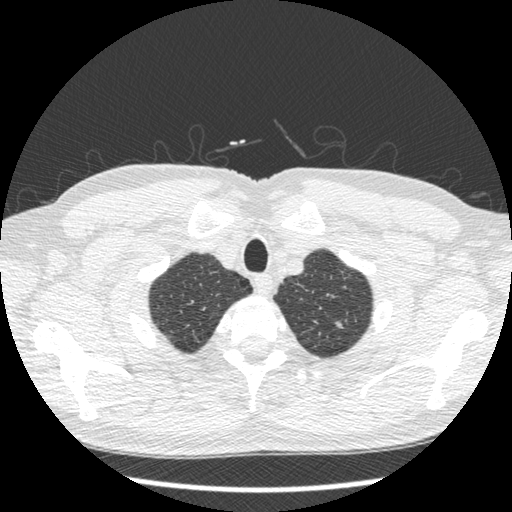
Low-dose screening chest CT, one axial slice. Position 405 of 439 along the scan axis. 120 kVp. Lung window (W 1500 / L -600 HU). 1.25 mm slice thickness. 512 × 512 image matrix, field of view 340 × 340 mm.
Structures marked on this image (outlined manually by an expert reader):
- lesion 1 (nodule, upper lobe of left lung): bounding box (x1, y1, x2, y2) in pixels: (335, 321, 344, 329)